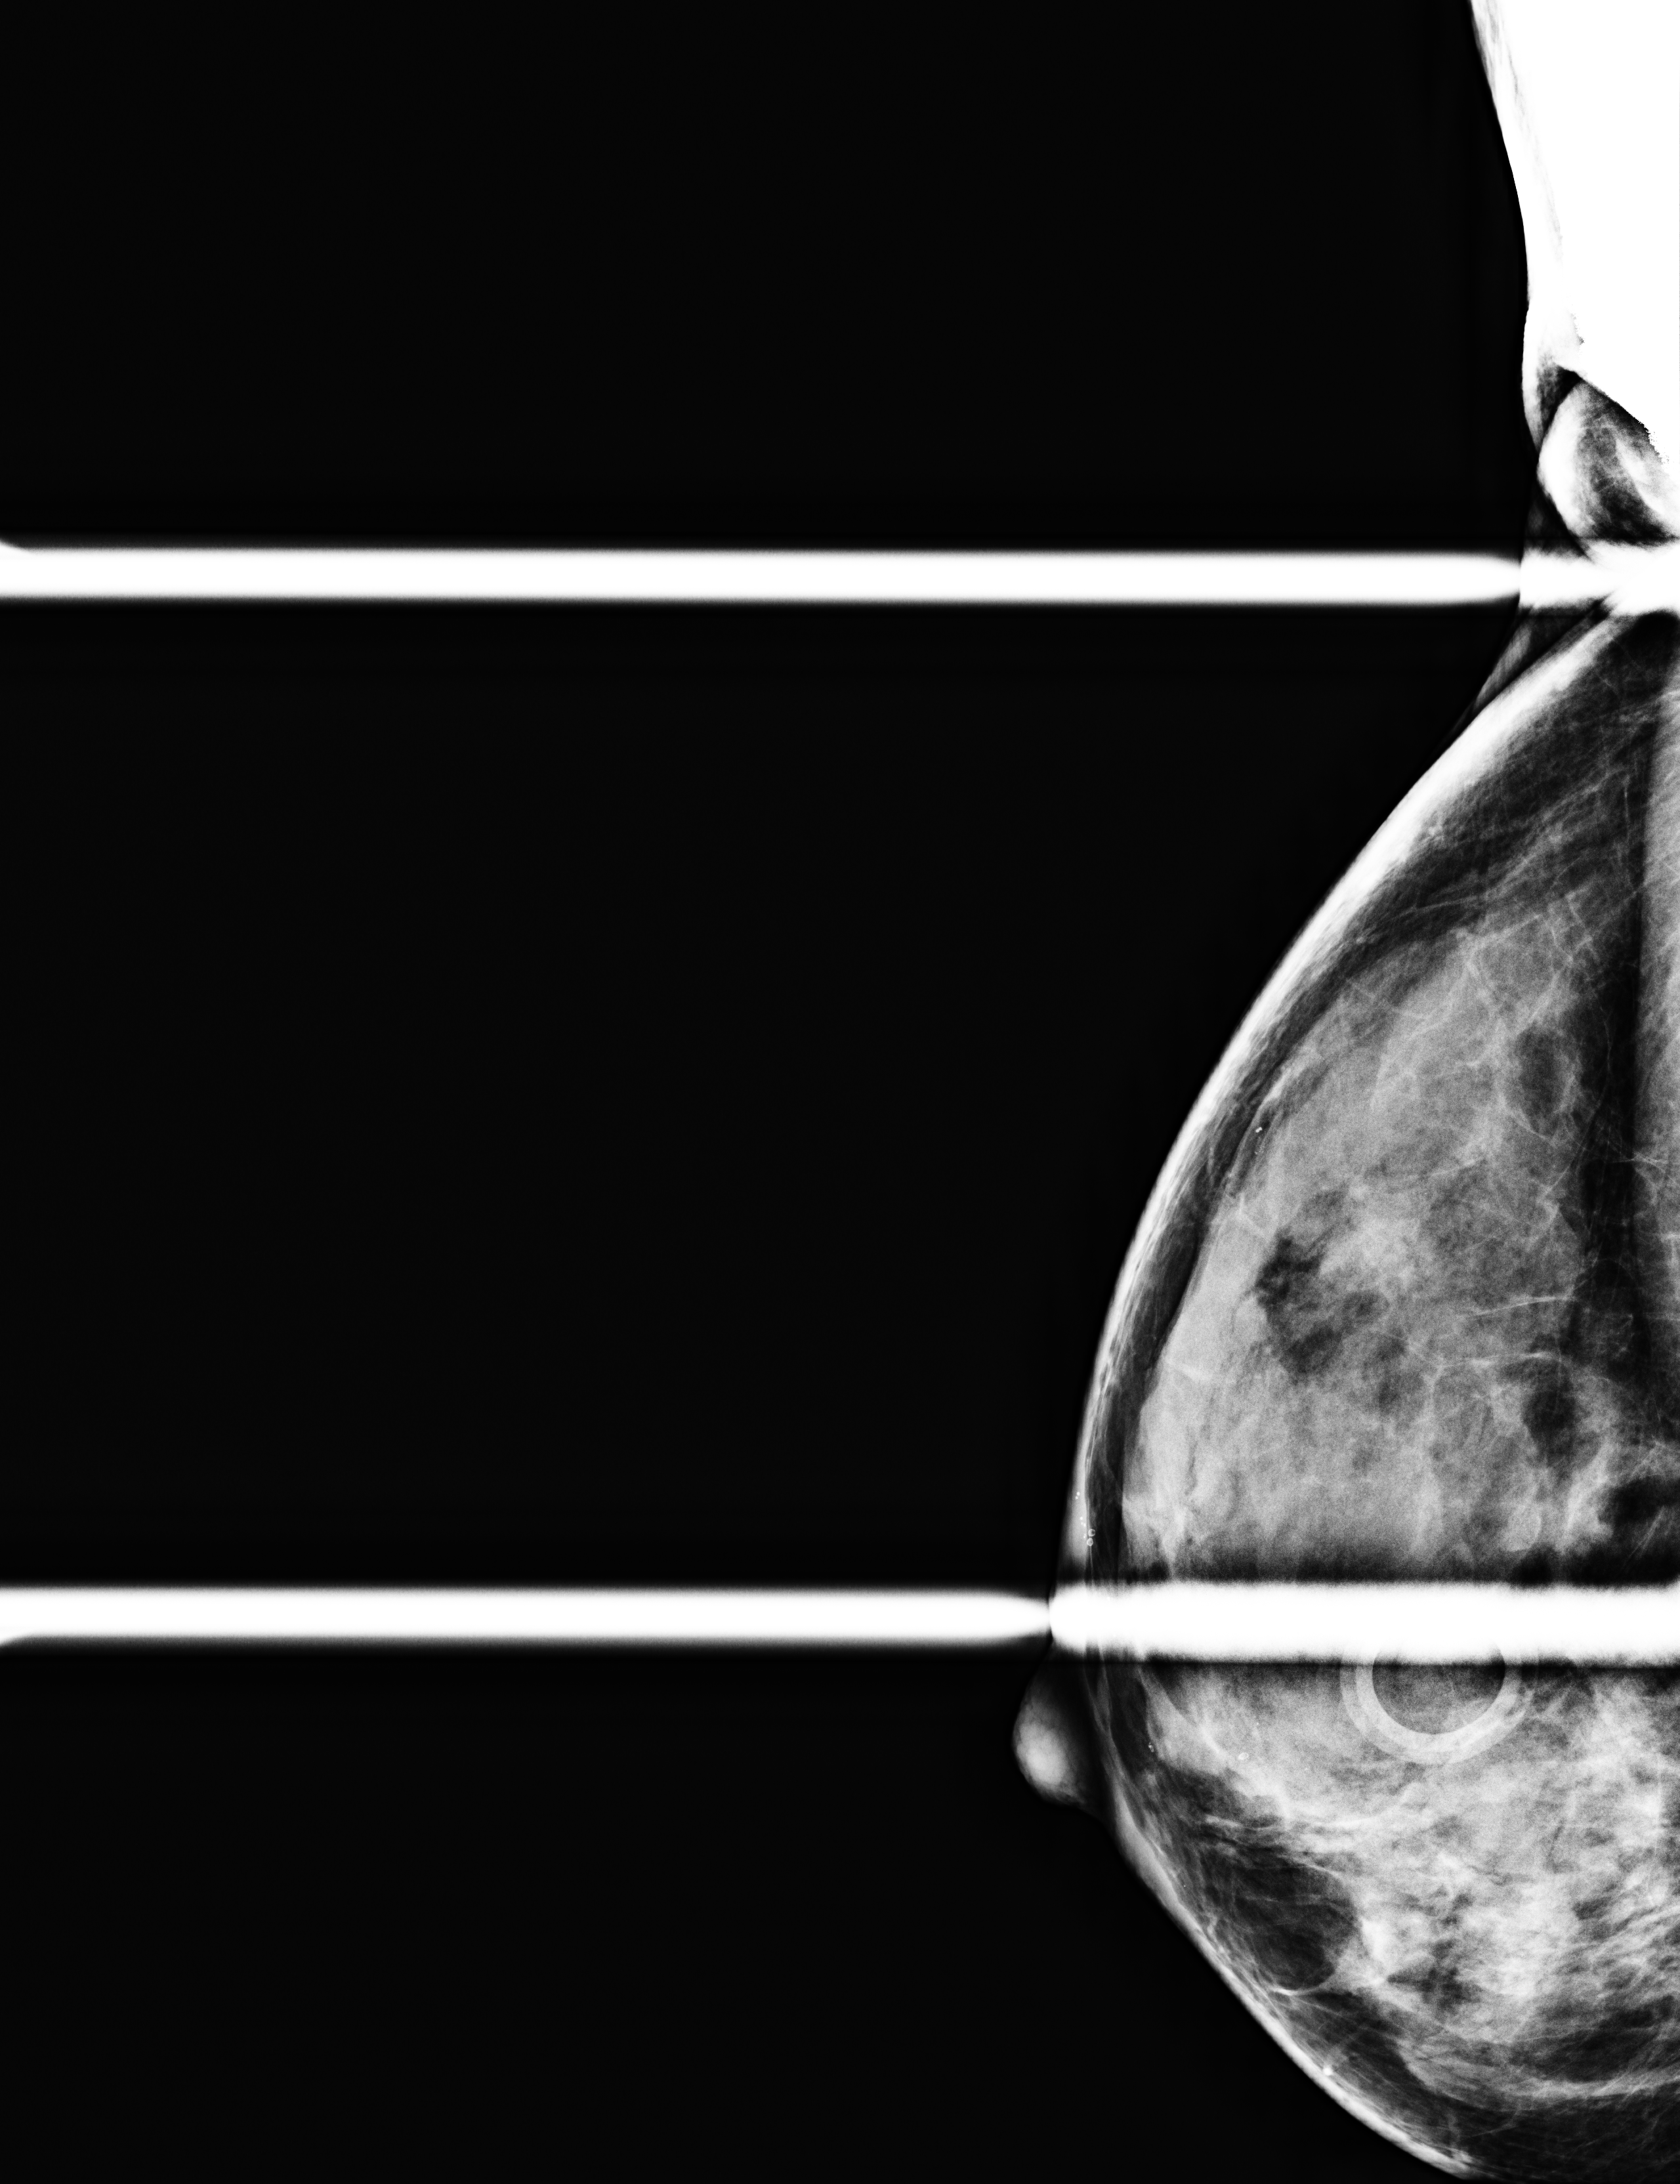
Additional work-up view. Patient: female, 56 years.
Image type: full-field digital mammogram. Breast: right. Projection: cranio-caudal projection, spot compression.